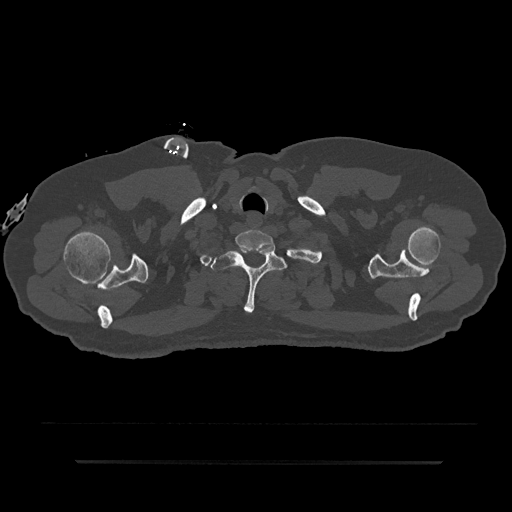
CT including the spine, one axial slice; reconstruction kernel Br40s/3; bone window (W 1800 / L 400 HU); 0.5 mm slice thickness; 512 × 512 image matrix, field of view 464 × 464 mm. Patient: male, 59 years. Case-level facts recorded for this patient, not image findings: primary cancer: bile ducts; vertebrae with lytic lesions (as recorded): T10.
Outlined on this slice (semi-automatically segmented with operator editing):
- T1 vertebra: box from (x=211, y=247) to (x=286, y=313) px